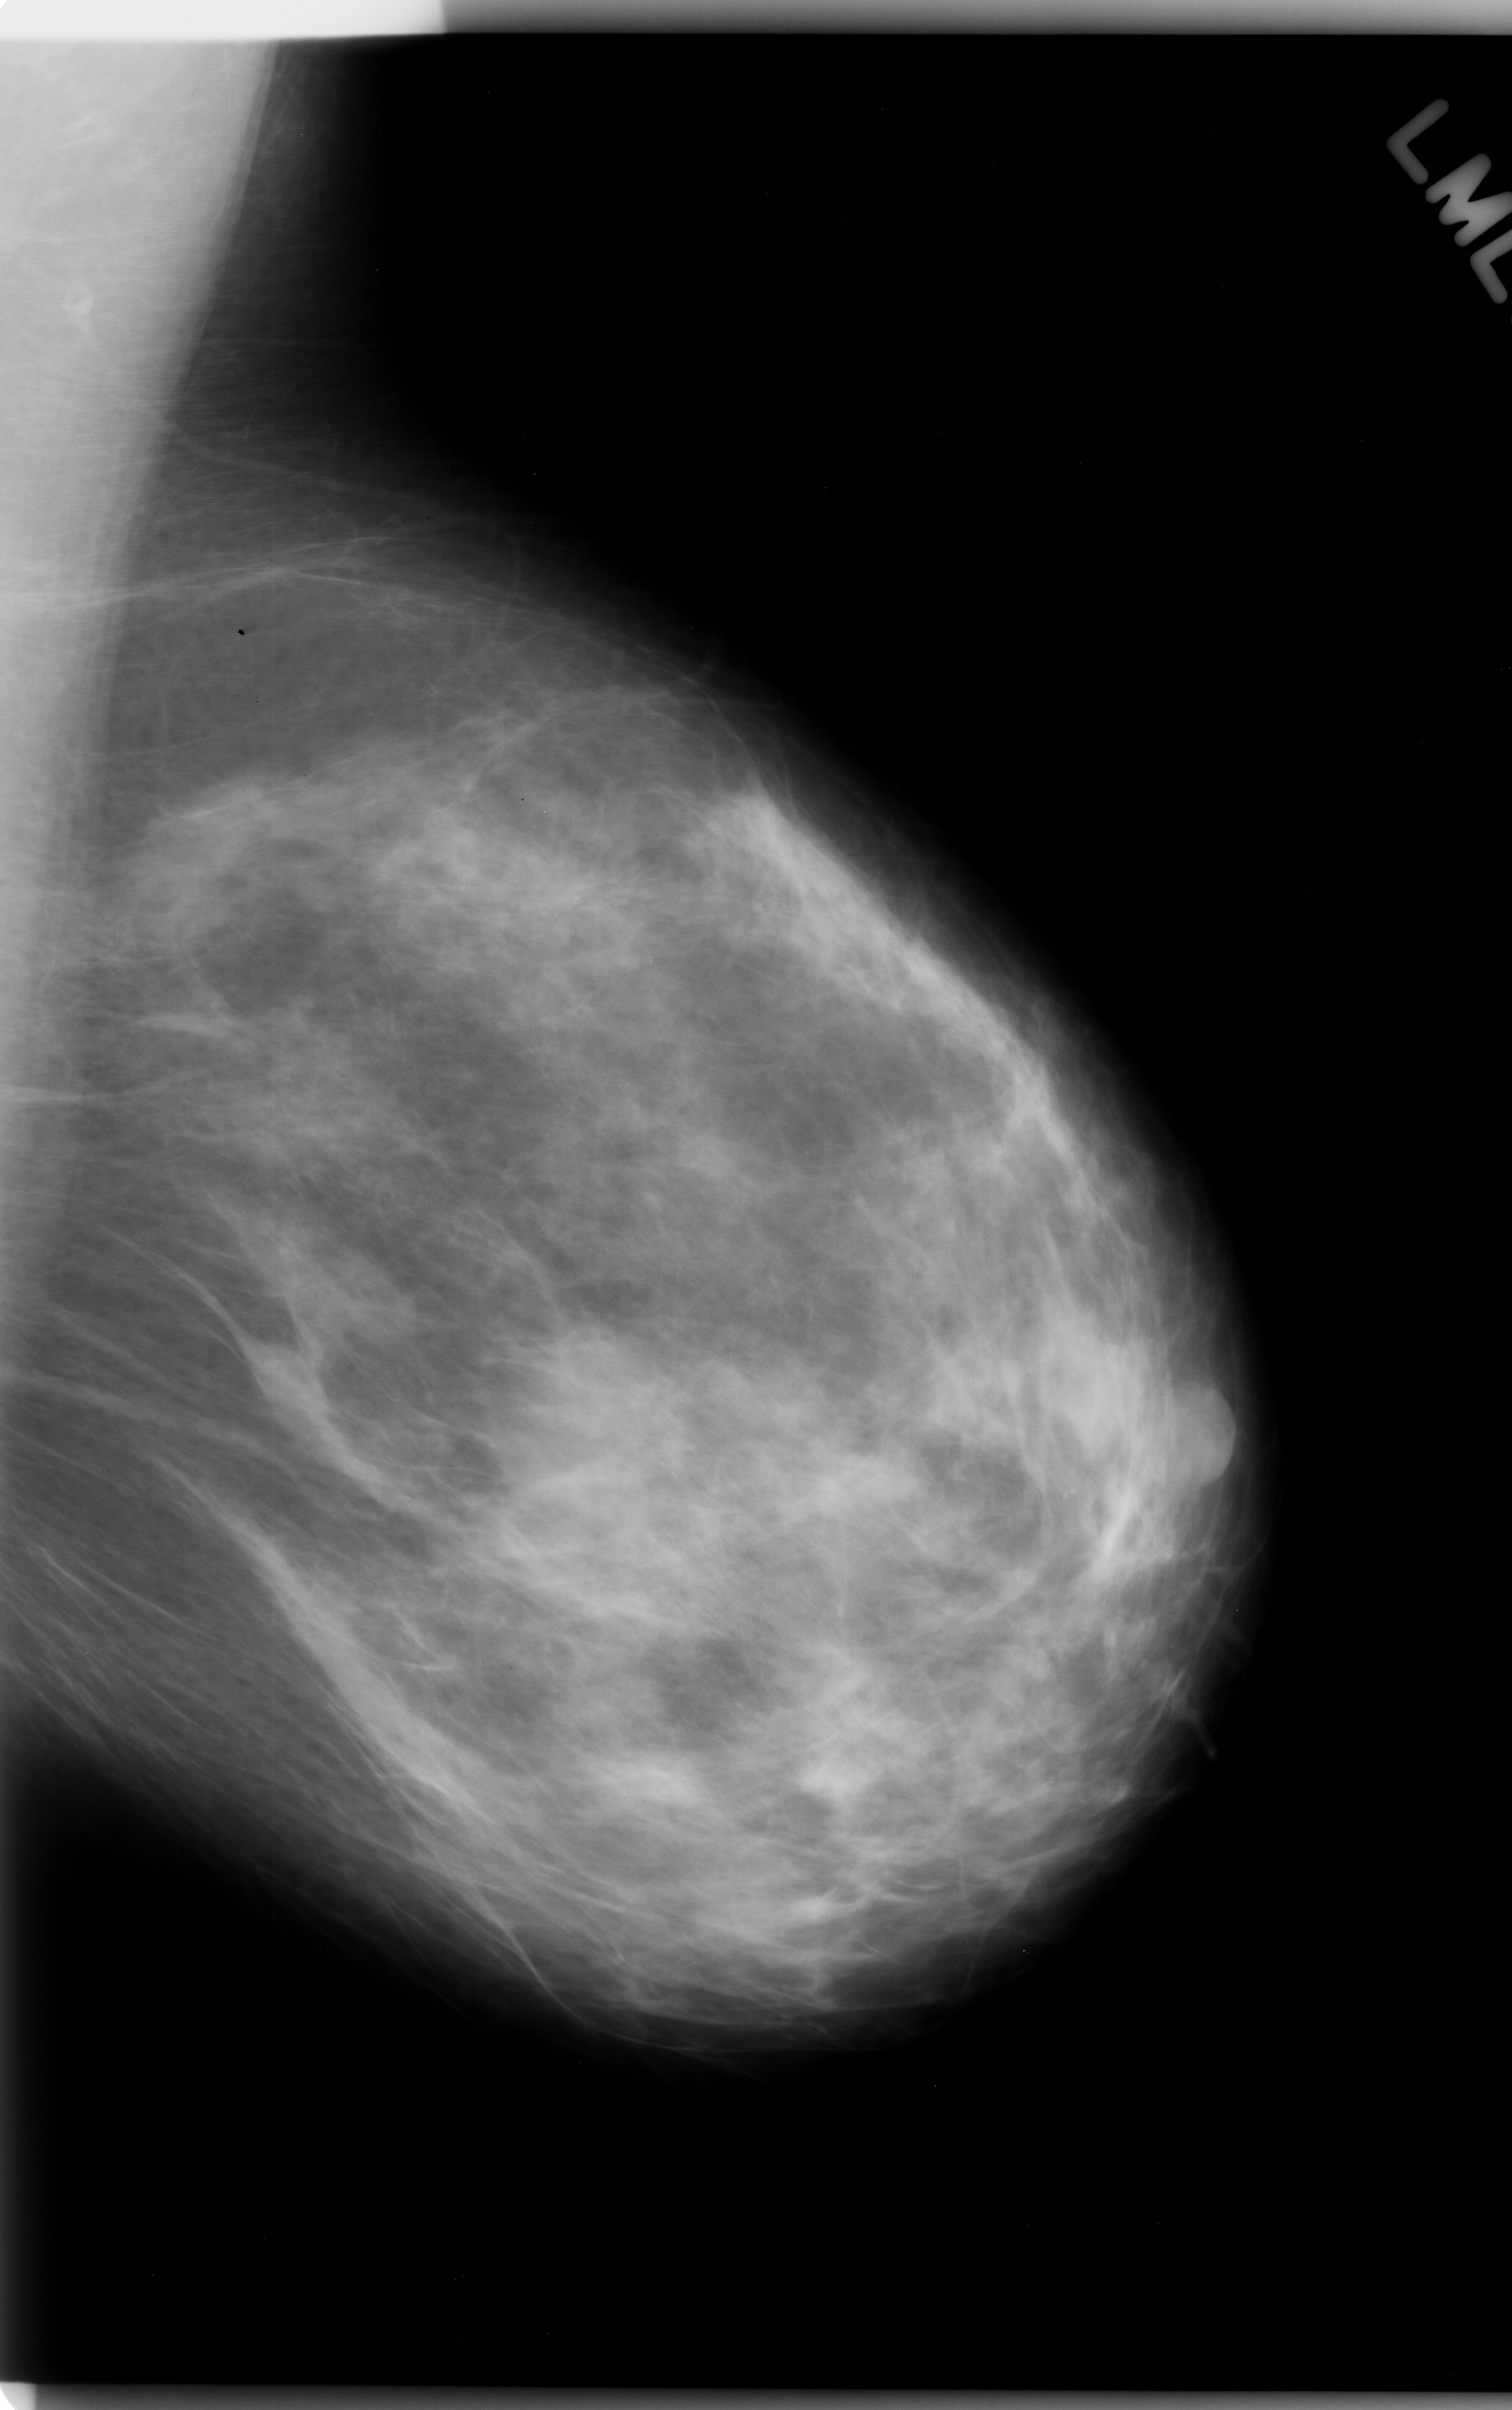
Scanned film-screen mammogram; left breast; mediolateral oblique (MLO) view; breast composition: scattered fibroglandular densities (BI-RADS density category 2 of 4).
- Calcifications, morphology pleomorphic, distribution clustered; BI-RADS assessment category 4; subtlety rating 3 on a 1 (subtle) to 5 (obvious) scale; pathology (as recorded): malignant.